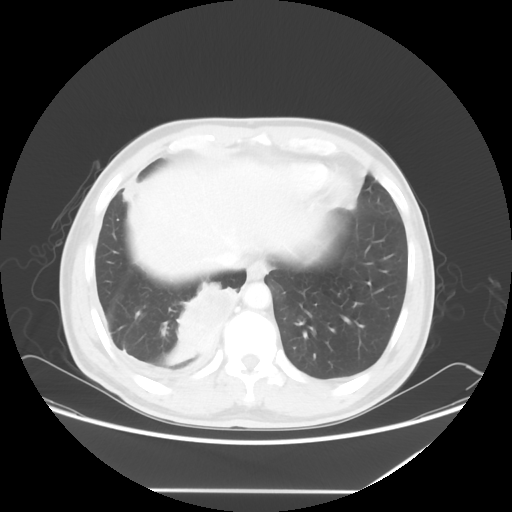
Chest CT, one axial slice; position 15 of 60 along the scan axis; 120 kVp; lung window (W 1500 / L -600 HU); 5 mm slice thickness; 512 × 512 image matrix. Patient: male, 48 years. From the clinical record (not read from this slice): clinical TNM (as recorded): T3 N3 M1a.
Annotated regions visible in this slice (rectangle marked by the reading radiologist):
- lung tumour (recorded histology: squamous cell carcinoma): bounding box (x1, y1, x2, y2) in pixels: (165, 278, 240, 368)